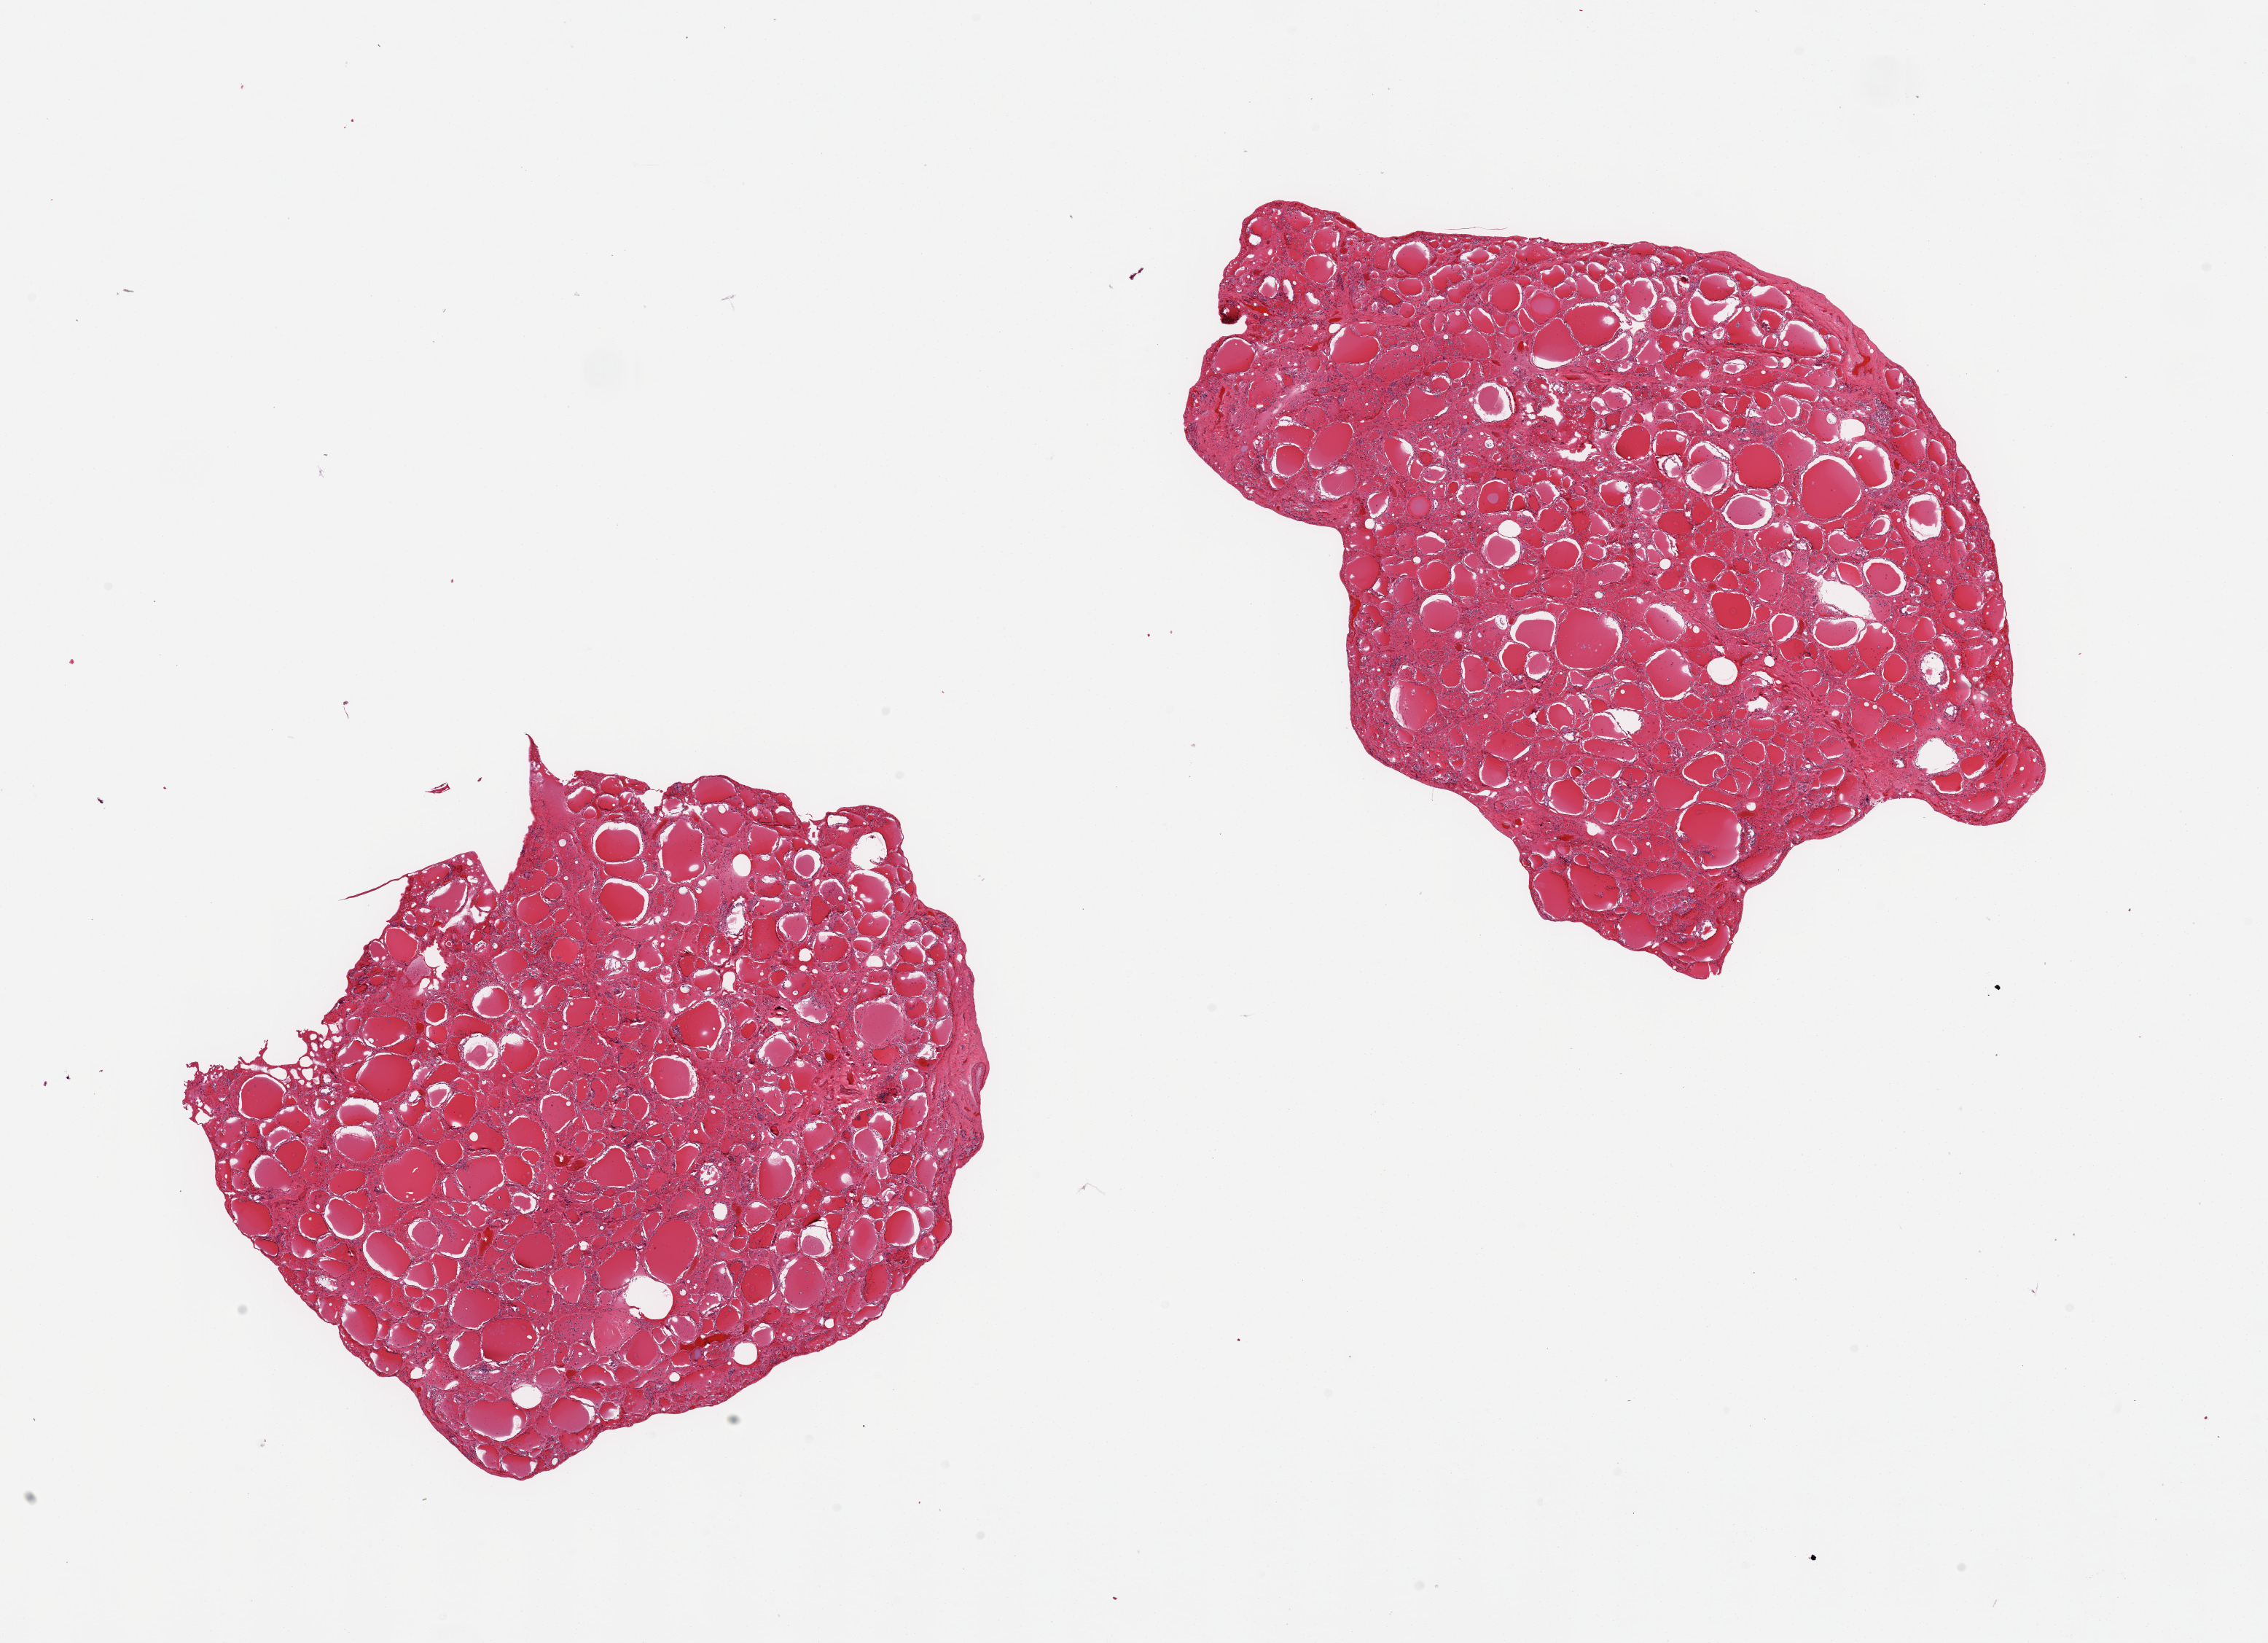
Hematoxylin and eosin (H&E) whole-slide image, shown as a low-resolution overview of the whole scanned area (about 24.6 x 17.8 mm). PAXgene-fixed, paraffin-embedded tissue. Sampled site (target tissue): thyroid. Donor tissue sample. Donor sex: male.
Reviewer comment on this tissue sample: 2 pieces; congestion.